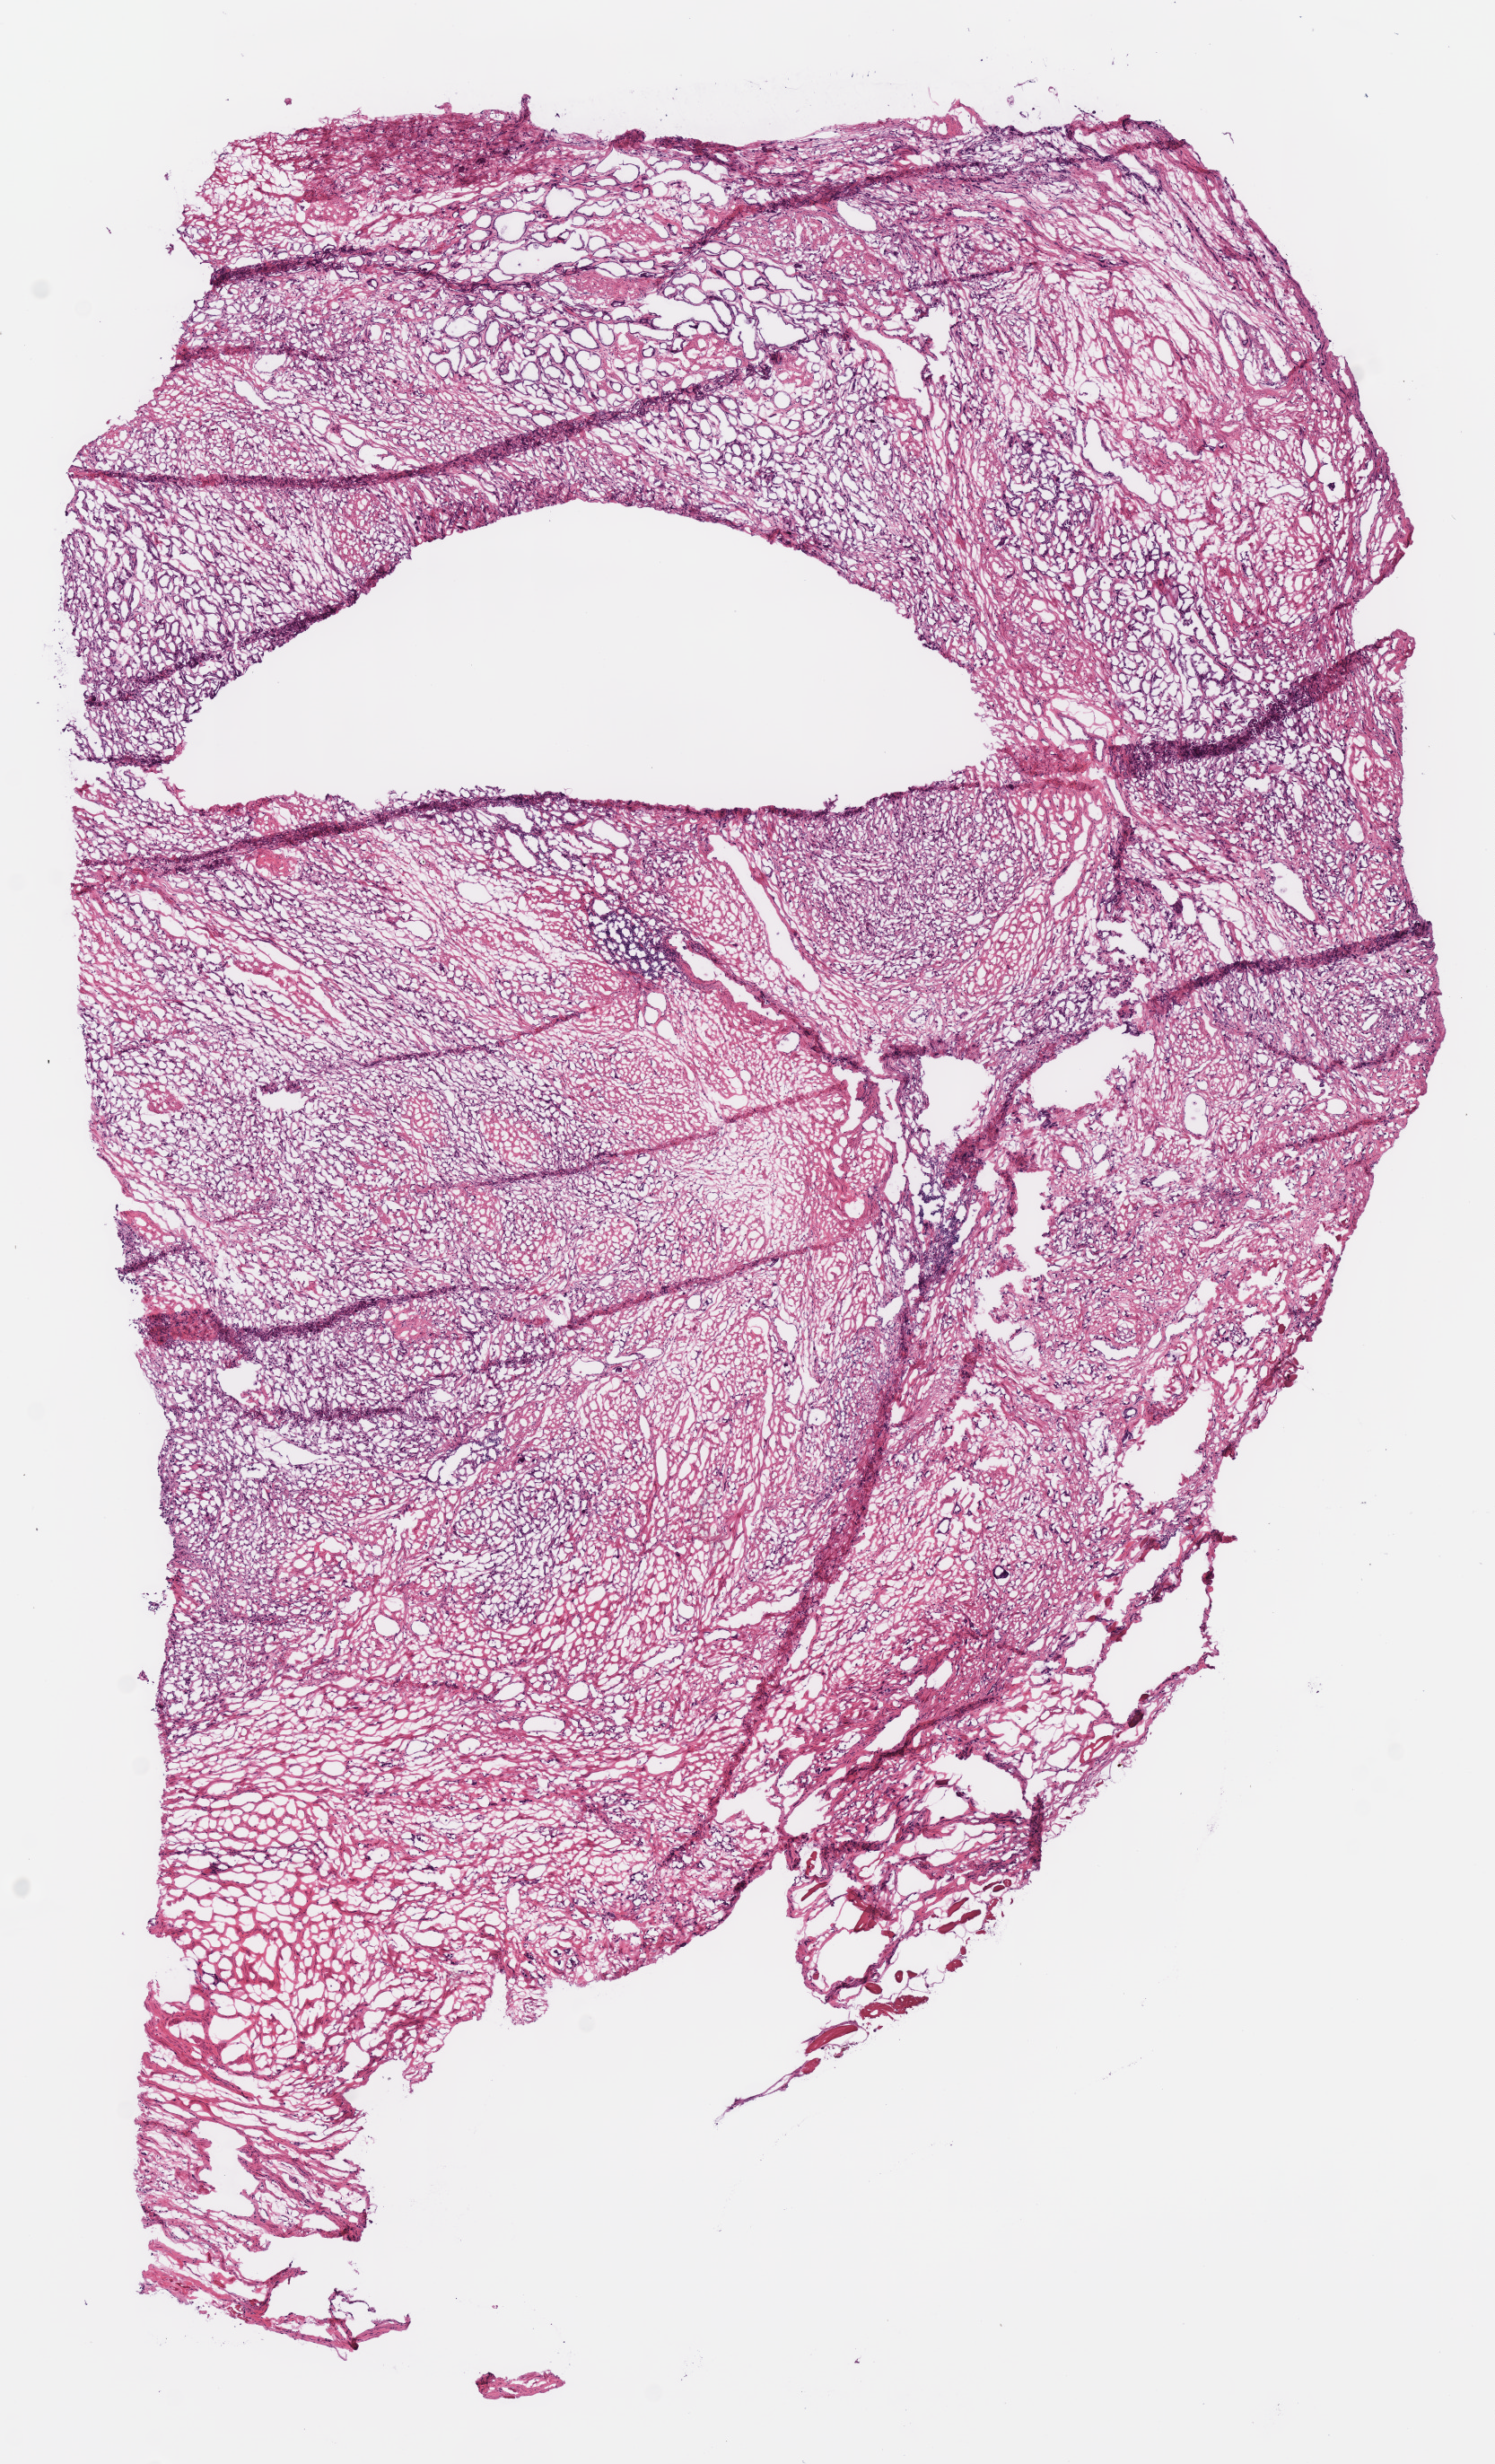
Digitized H&E tissue section (whole slide), low-resolution overview of the scanned area, about 6.6 x 10.8 mm (slide scanned at 40x); frozen section; prostate, primary tumour sample. Patient: male, age at initial diagnosis 44 years.
Pathologic diagnosis: Acinar cell carcinoma (prostate gland).